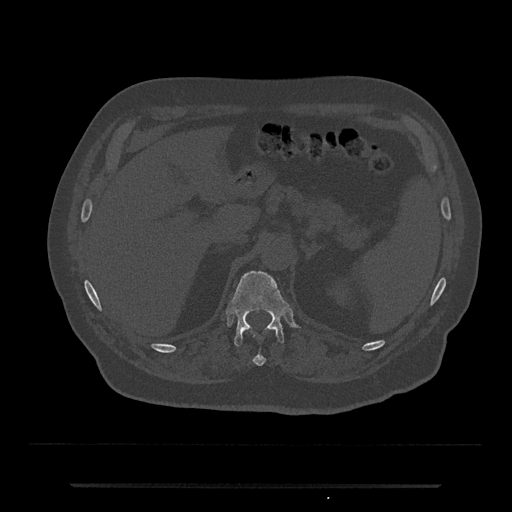
CT including the spine, one axial slice. Position 609 of 797 along the scan axis. Reconstruction kernel Br40s/3. Bone window (W 1800 / L 400 HU). 0.5 mm slice thickness. 512 × 512 image matrix, field of view 434 × 434 mm. Patient: male, 80 years. Case-level facts recorded for this patient, not image findings: primary cancer: prostate; vertebrae with lytic lesions (as recorded): L1, T11.
Structures marked on this image (semi-automatically segmented with operator editing):
- T11 vertebra: bounding box (x1, y1, x2, y2) in pixels: (253, 356, 266, 366)
- T12 vertebra: (228, 271, 289, 346)